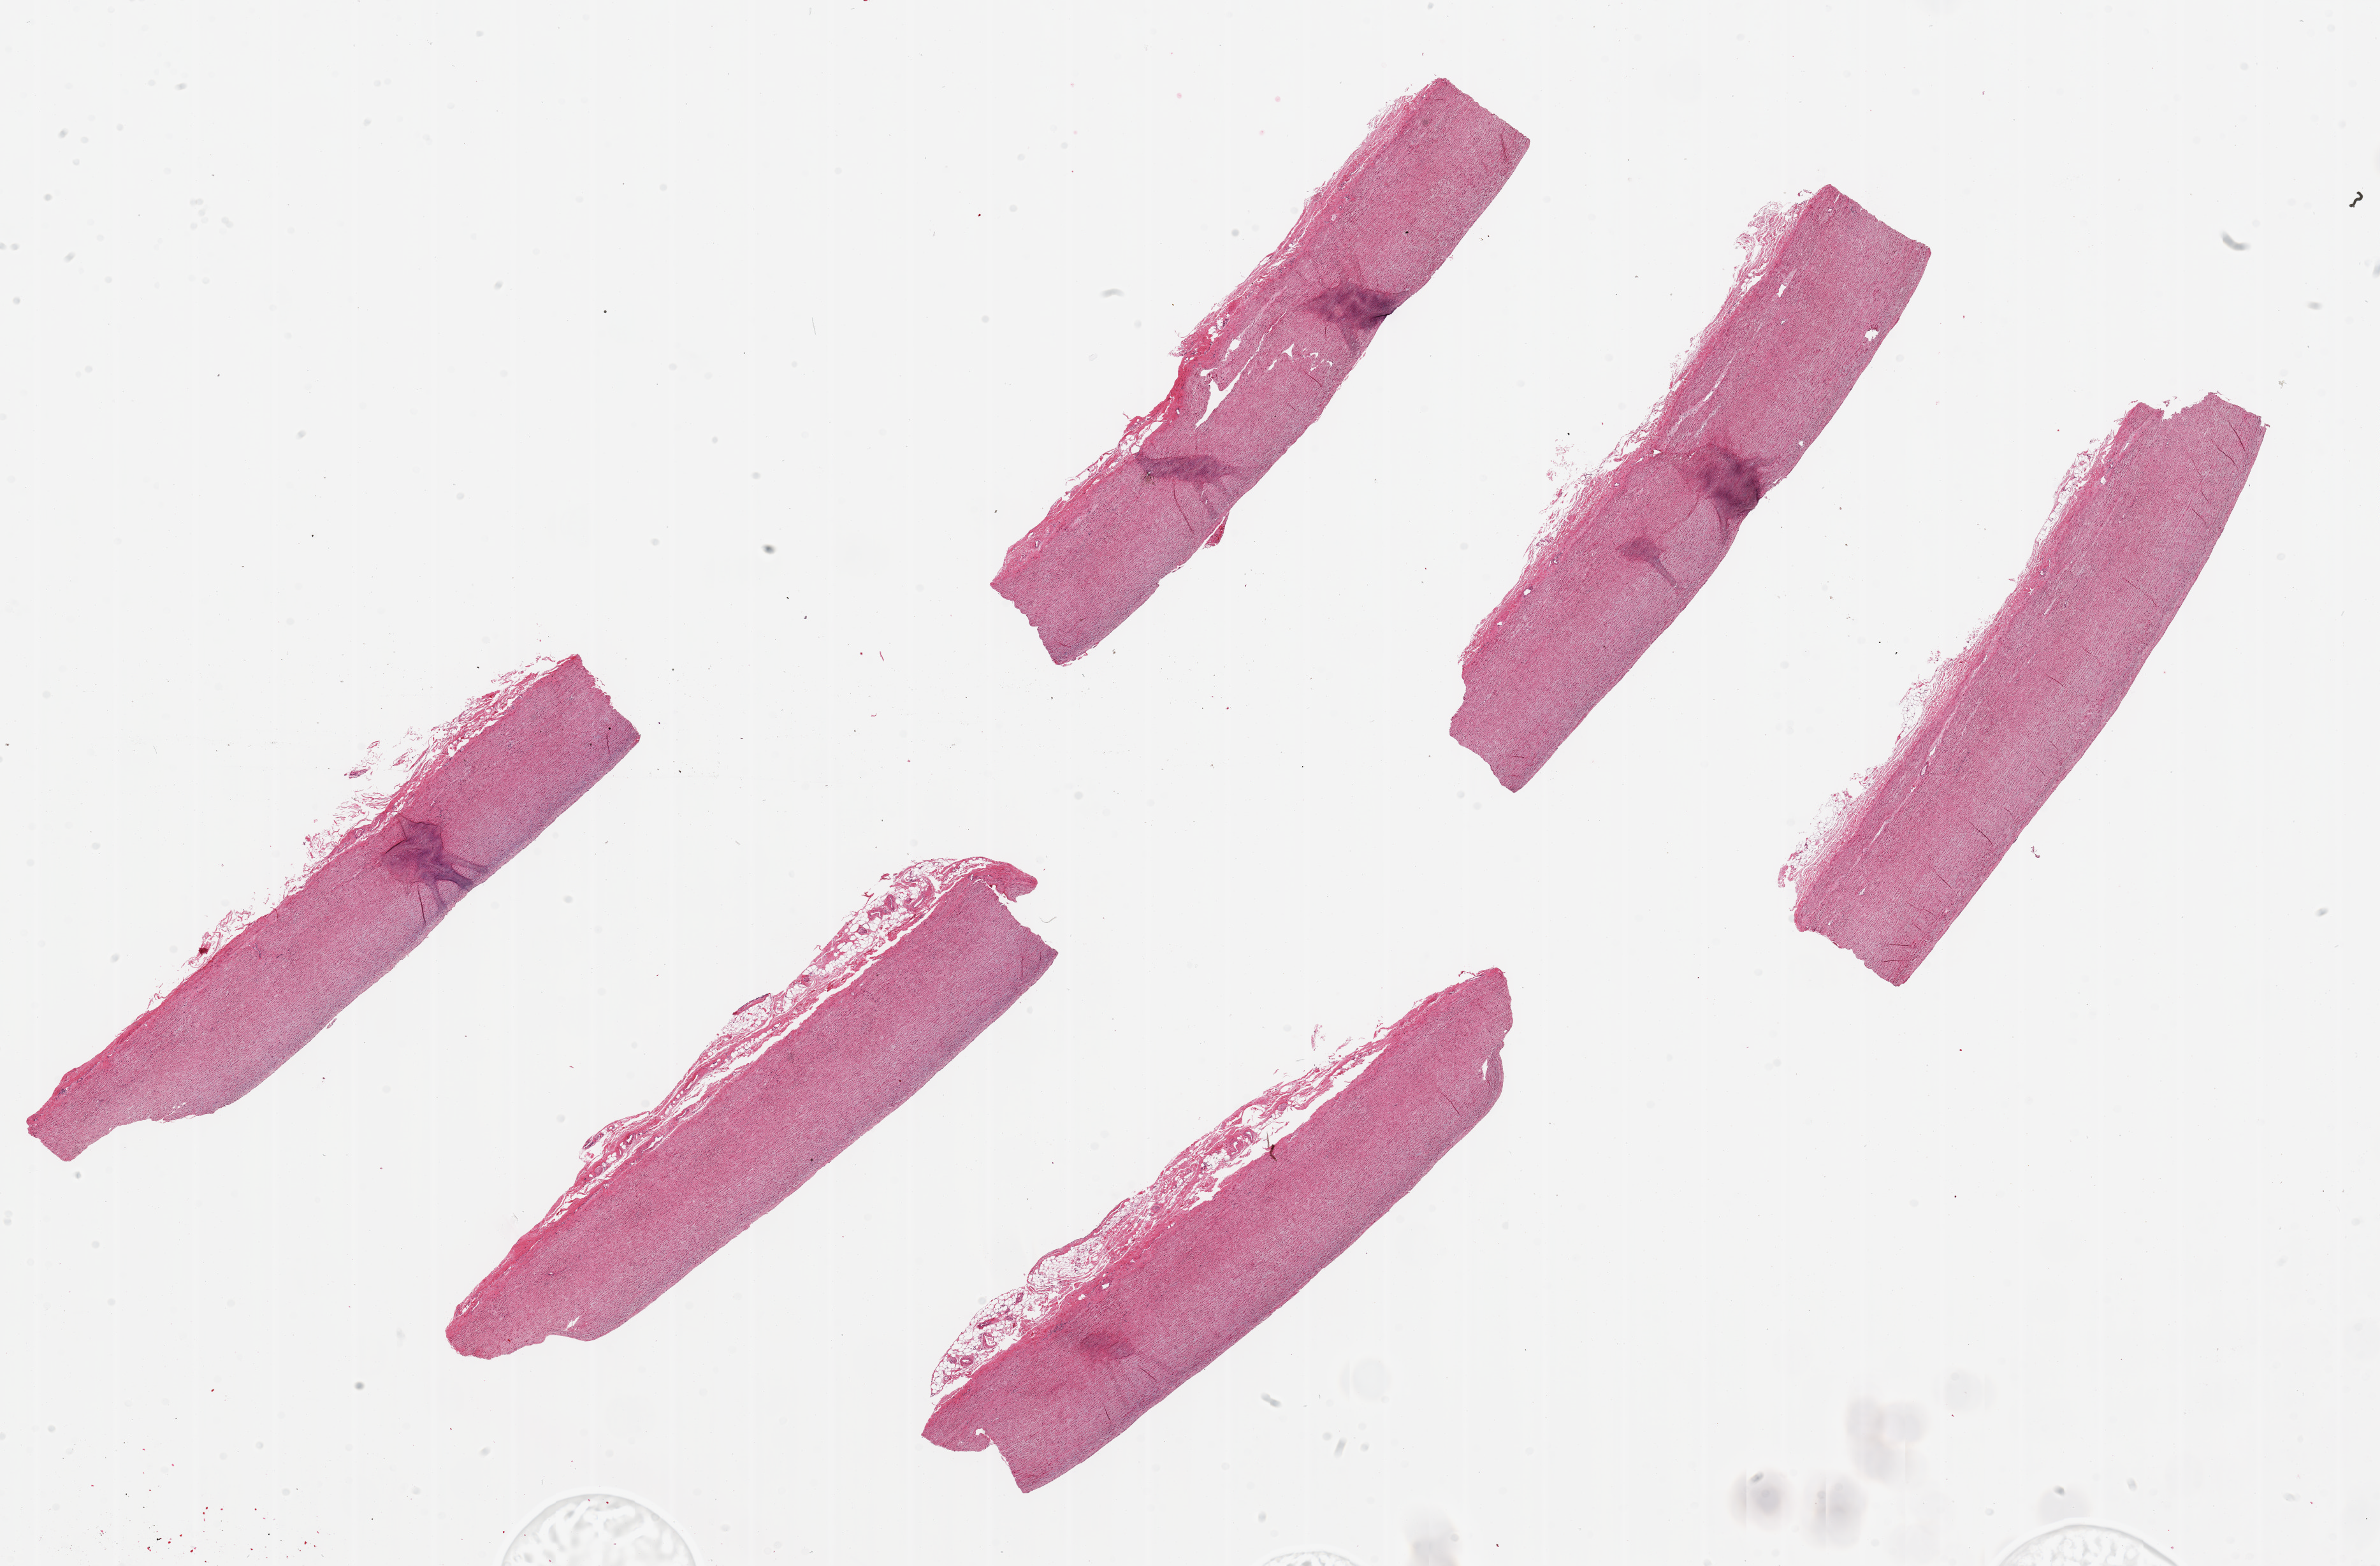
Whole-slide image, hematoxylin and eosin (H&E) stain — a low-resolution overview of the entire scanned area, about 29.5 x 19.4 mm (from a 20x scan), PAXgene-fixed paraffin-embedded (PFPE) section, section of aorta (target tissue), donor tissue sample. Donor: male.
Reviewer comment on this tissue sample: 6 pieces, ~9x1.5.